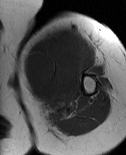
MRI of an extremity soft-tissue mass, one axial slice; slice 53 of 86 in the series (ordered by position); MR volume resampled by the dataset authors to the PET/CT grid (not the native acquisition matrix); 3.27 mm slice thickness; 126 × 155 image matrix, field of view 123 × 151 mm. Female patient. From the clinical record (not read from this slice): histological type: pleiomorphic leiomyosarcoma; grade: high; site of the primary tumour: left biceps.
Annotated regions visible in this slice (expert contour drawn on MRI and transferred to this co-registered scan by the dataset authors):
- gross tumour volume including surrounding oedema: bounding box [x1, y1, x2, y2] px = [22, 24, 89, 116]
- gross tumour volume (mass): [22, 26, 85, 105]